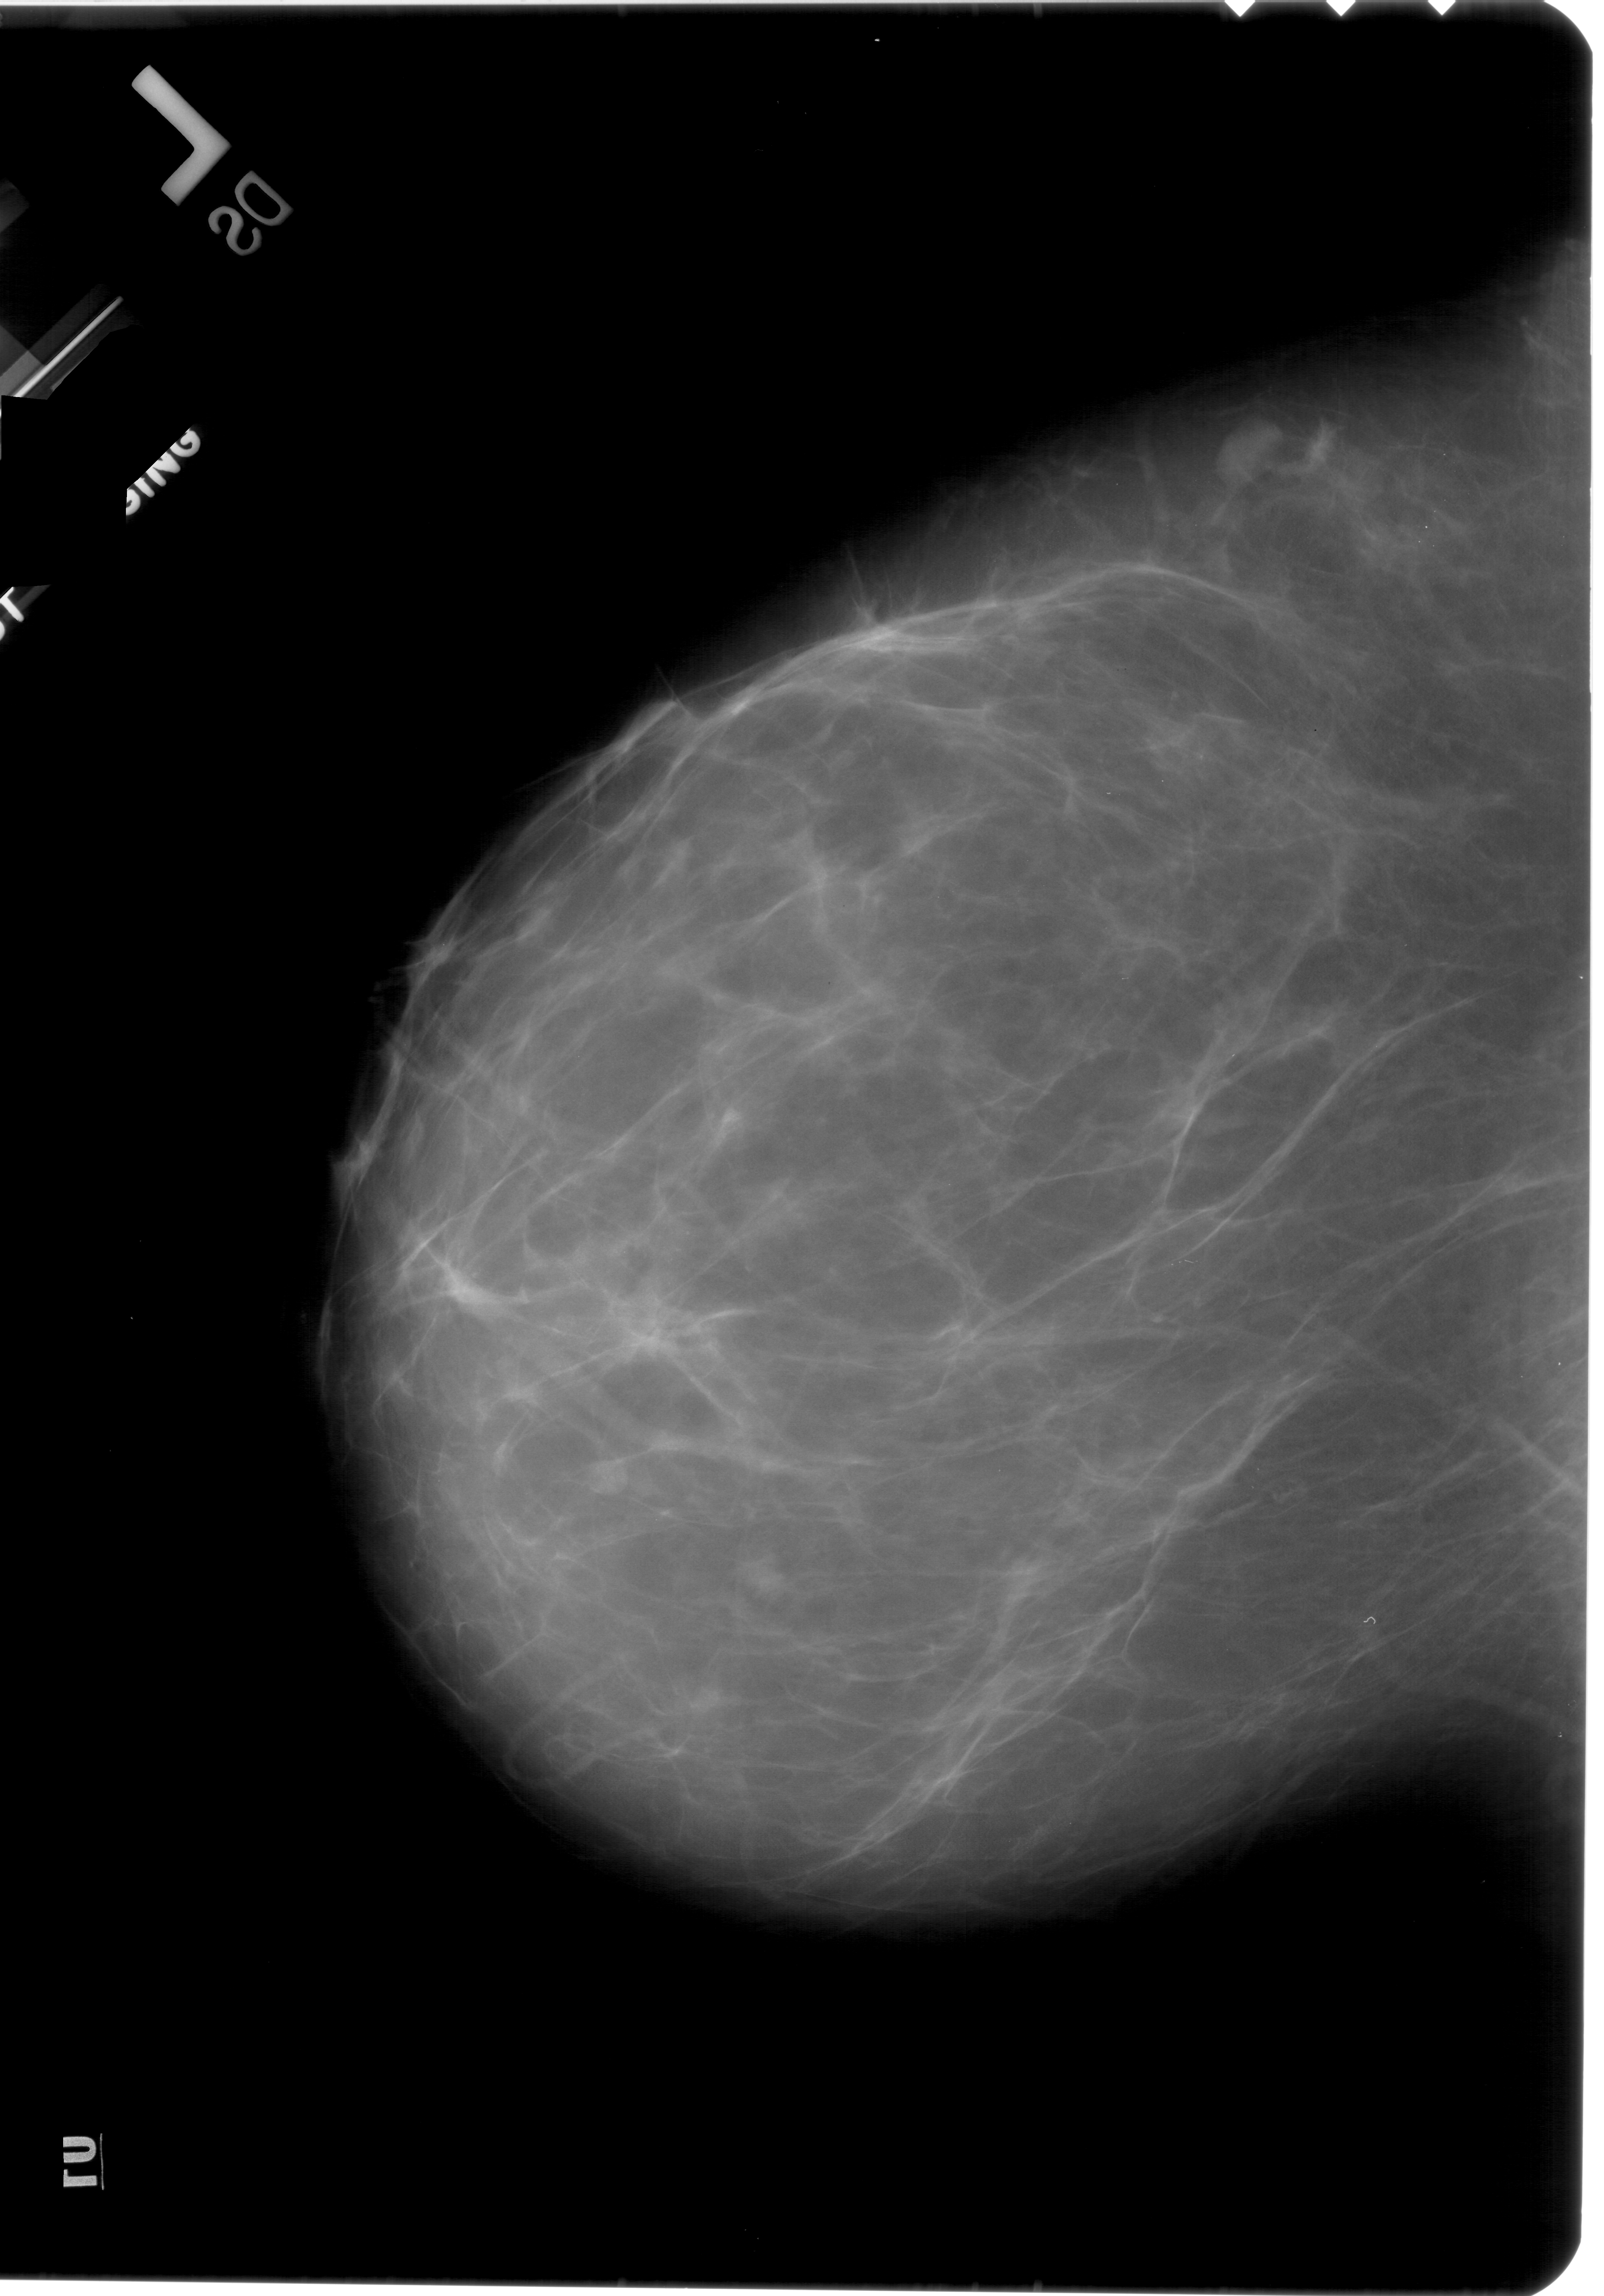
Scanned film-screen mammogram; left breast; craniocaudal (CC) view; BI-RADS breast density category 2 (scale 1–4).
- Radiologist-marked abnormalities on this image: calcifications, morphology pleomorphic, distribution clustered; BI-RADS assessment category 4; pathology result (as recorded, not read from the image): benign.